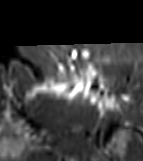
MRI of an extremity soft-tissue mass, one axial slice. Position 50 of 81 along the scan axis. STIR. MR volume resampled by the dataset authors to the PET/CT grid (not the native acquisition matrix). 3.27 mm slice thickness. 143 × 161 image matrix, field of view 140 × 157 mm. Female patient. Case-level facts recorded for this patient, not image findings: histological type: myxofibrosarcoma; grade: intermediate; site of the primary tumour: left thigh.
Annotated regions visible in this slice (expert contour drawn on MRI and transferred to this co-registered scan by the dataset authors):
- gross tumour volume including surrounding oedema: bounding box (x1, y1, x2, y2) in pixels: (28, 67, 118, 107)